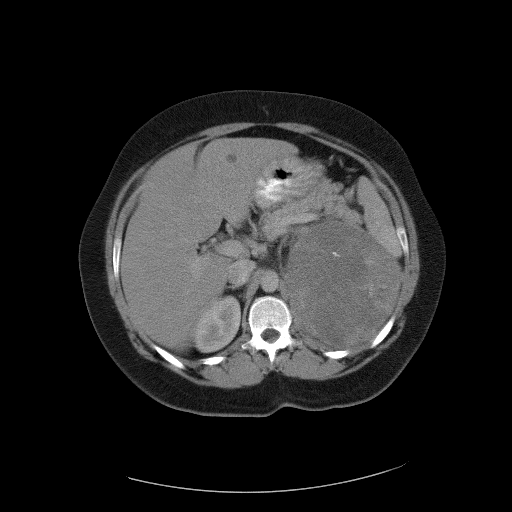
Contrast-enhanced abdominal CT, one axial slice. Slice 69 of 90 in the series (ordered by position). Reconstruction kernel FC01. Intravenous contrast given. Soft-tissue window (W 400 / L 40 HU). 512 × 512 image matrix. Female patient, age 55 years. From the clinical record (not read from this slice): diagnosis: adrenocortical carcinoma; tumour side: left adrenal; tumour size at pathology: 22 cm; Ki-67 index: 10 %; stage (as recorded): 3.
Structures marked on this image (semi-automatic segmentation, software-assisted and operator-edited):
- mass: box from (x=291, y=223) to (x=397, y=347) px